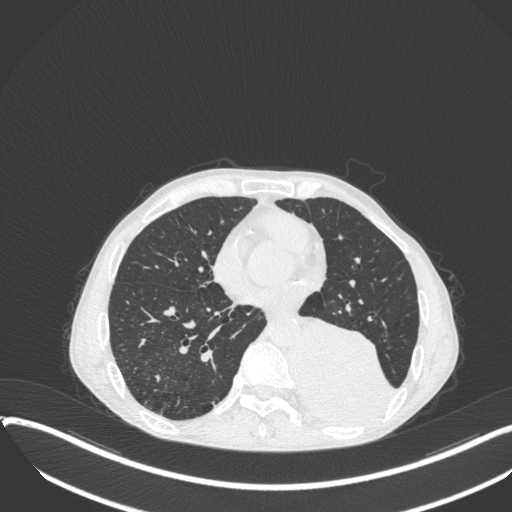
Chest CT, one axial slice; position 144 of 400 along the scan axis; reconstruction kernel B31f; lung window (W 1500 / L -600 HU); 1 mm slice thickness; 512 × 512 image matrix. Patient: male, 57 years. From the clinical record (not read from this slice): clinical TNM (as recorded): T4 N0 M0.
Annotated regions visible in this slice (bounding box drawn by a radiologist):
- lung tumour (recorded histology: squamous cell carcinoma): bounding box [x1, y1, x2, y2] px = [288, 309, 397, 432]